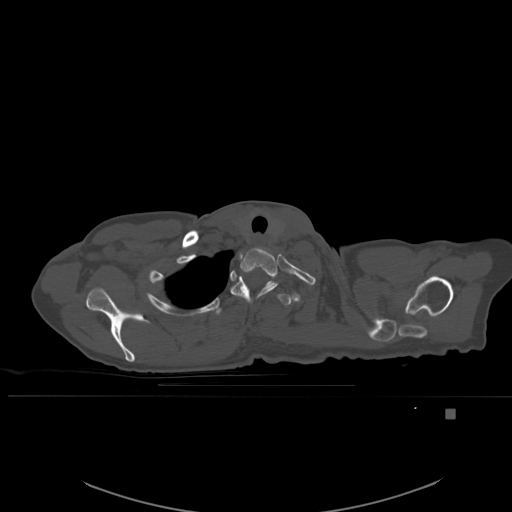
CT including the spine, one axial slice. Position 441 of 537 along the scan axis. Bone window (W 1800 / L 400 HU). 1.5 mm slice thickness. 512 × 512 image matrix. Patient: female, 45 years. From the clinical record (not read from this slice): primary cancer: lung.
Structures marked on this image (semi-automatically segmented with operator editing):
- T1 vertebra: bounding box [x1, y1, x2, y2] px = [239, 247, 277, 280]
- T2 vertebra: [230, 279, 289, 311]
- T3 vertebra: [214, 306, 222, 316]